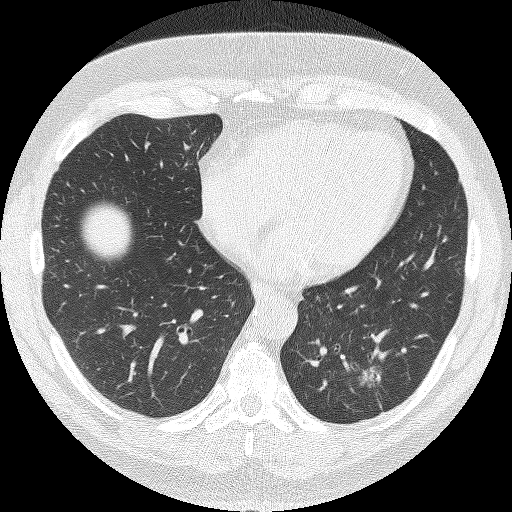
Chest CT (low-dose screening protocol), one axial image; first (baseline) screen; lung window (W 1500 / L -600 HU); 2 mm slice thickness; lung (sharp) reconstruction kernel (FC51); slice 94 of 140 in the series. Male, age 62 years at enrolment.
Lesion marked by an expert reader, bounding box [x1, y1, x2, y2] px = [347, 354, 404, 410]. The screening reader recorded 2 non-calcified nodules or masses ≥4 mm on this exam (left lower lobe, right upper lobe); which of them this box marks is not recorded. Lung cancer was diagnosed 90 days after this screen: adenocarcinoma, NOS, left lower lobe, moderately differentiated (G2), stage IA (AJCC 6th edition), 30 mm at pathology.